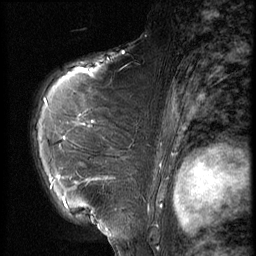
Breast MRI (dynamic contrast-enhanced), one sagittal slice; position 43 of 56 along the scan axis; 3 images stored at this slice position (order not interpretable as contrast timing); 1.5 T; TE 4.2 ms, TR 9 ms; 2.5 mm slice thickness; 256 × 256 image matrix, field of view 180 × 180 mm. Female patient, age 61 years. Case-level facts recorded for this patient, not image findings: setting: breast cancer imaged before/during neoadjuvant chemotherapy; receptor status: HR-positive, HER2-negative.
Structures marked on this image (semi-automatically segmented with operator editing):
- analysis volume of interest (the breast-tissue region the enhancement analysis was run in; not a lesion): bounding box [x1, y1, x2, y2] px = [47, 89, 153, 191]
- tumour enhancement mask (voxels above the 140 % enhancement threshold inside the analysis volume of interest): [50, 176, 62, 187]